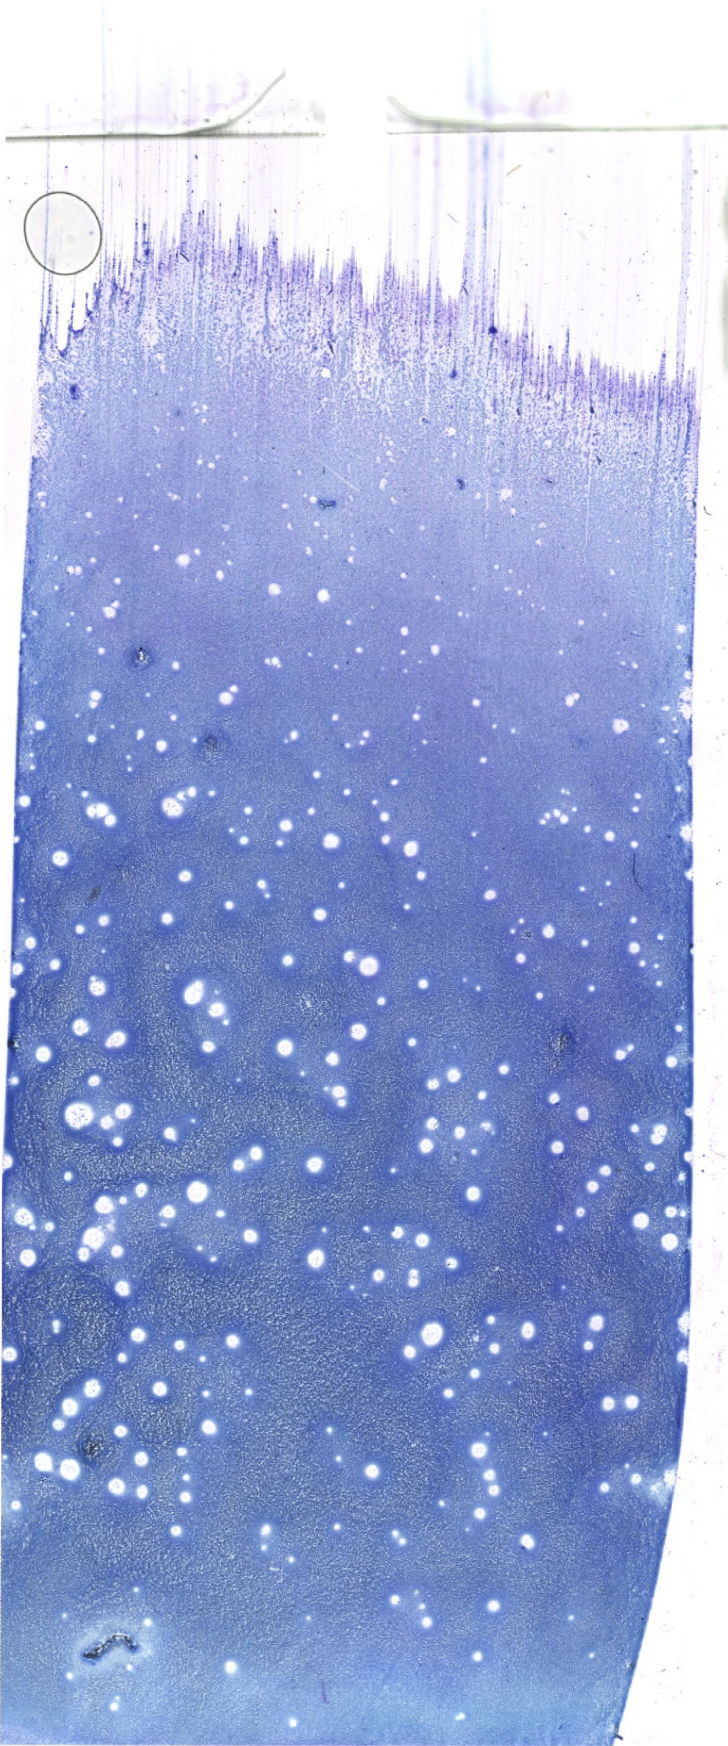
Bone marrow aspirate smear, May-Grünwald-Giemsa (MGG) stain, whole-slide image — a low-resolution overview of the entire scanned area, about 20.6 x 49.5 mm. Female patient.
Diagnosis: Acute Myeloid Leukemia without Maturation.